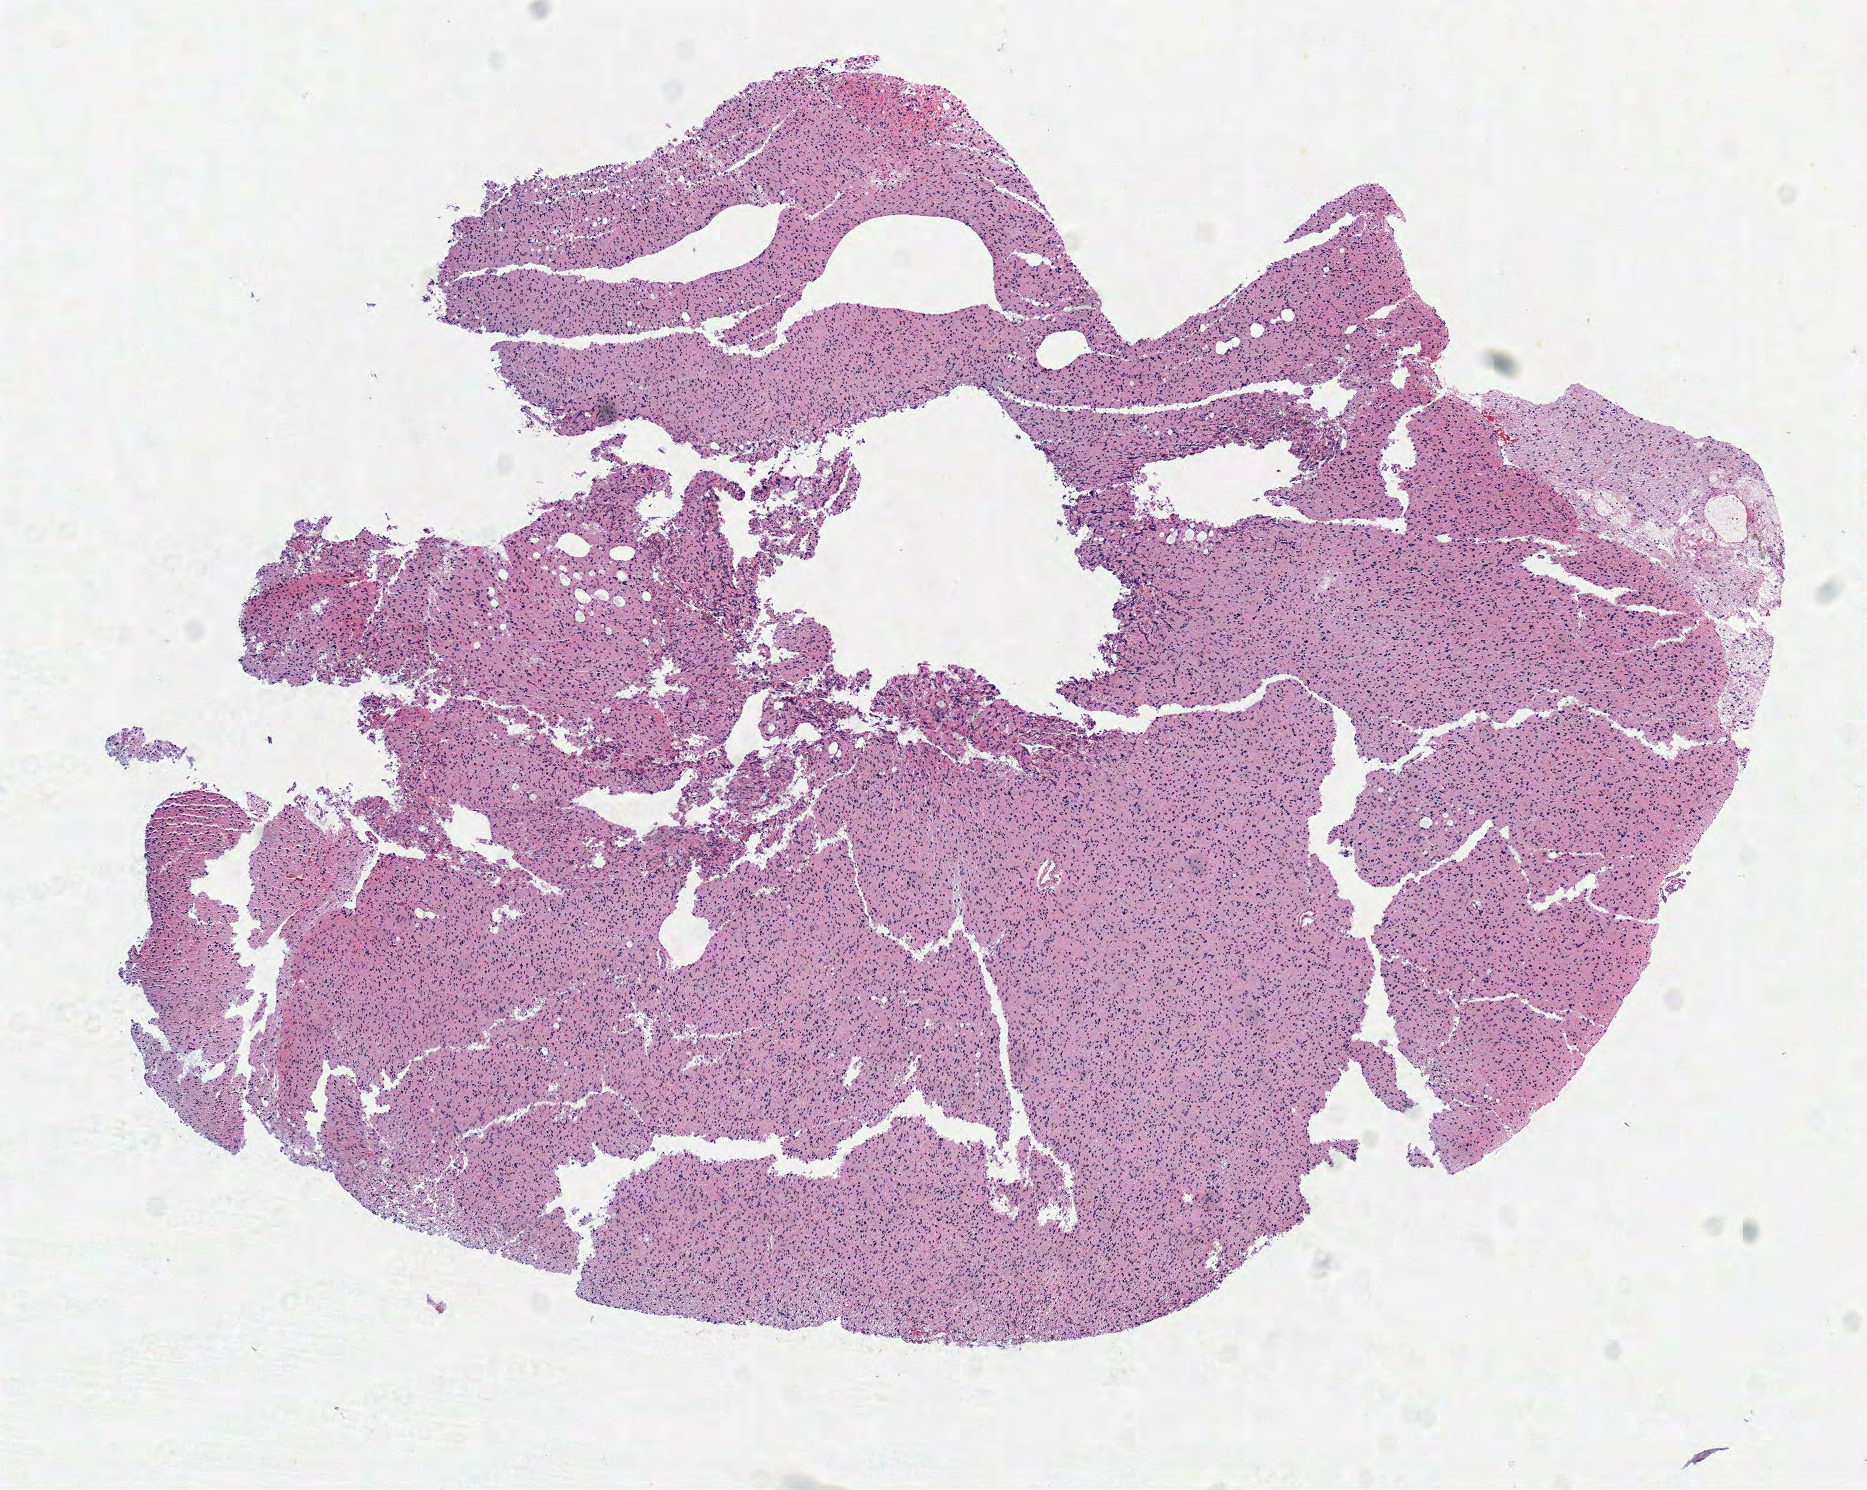
Digitized Hematoxylin and eosin (H&E) stained tissue section (whole slide), shown as a low-resolution overview of the whole scanned area (about 7.3 x 5.9 mm, acquisition: 40x scan), frozen section from the top of the tissue portion, brain, primary tumour sample. Female, age 23 years at initial diagnosis. Histologic grade: G3 (poorly differentiated). Pathologist review of this section (percent, as recorded): tumour cells 100%, tumour nuclei 75%, normal cells 0%, stromal cells 0%, necrosis 0%.
Laterality: right. Diagnosis: Oligodendroglioma, anaplastic (cerebrum).